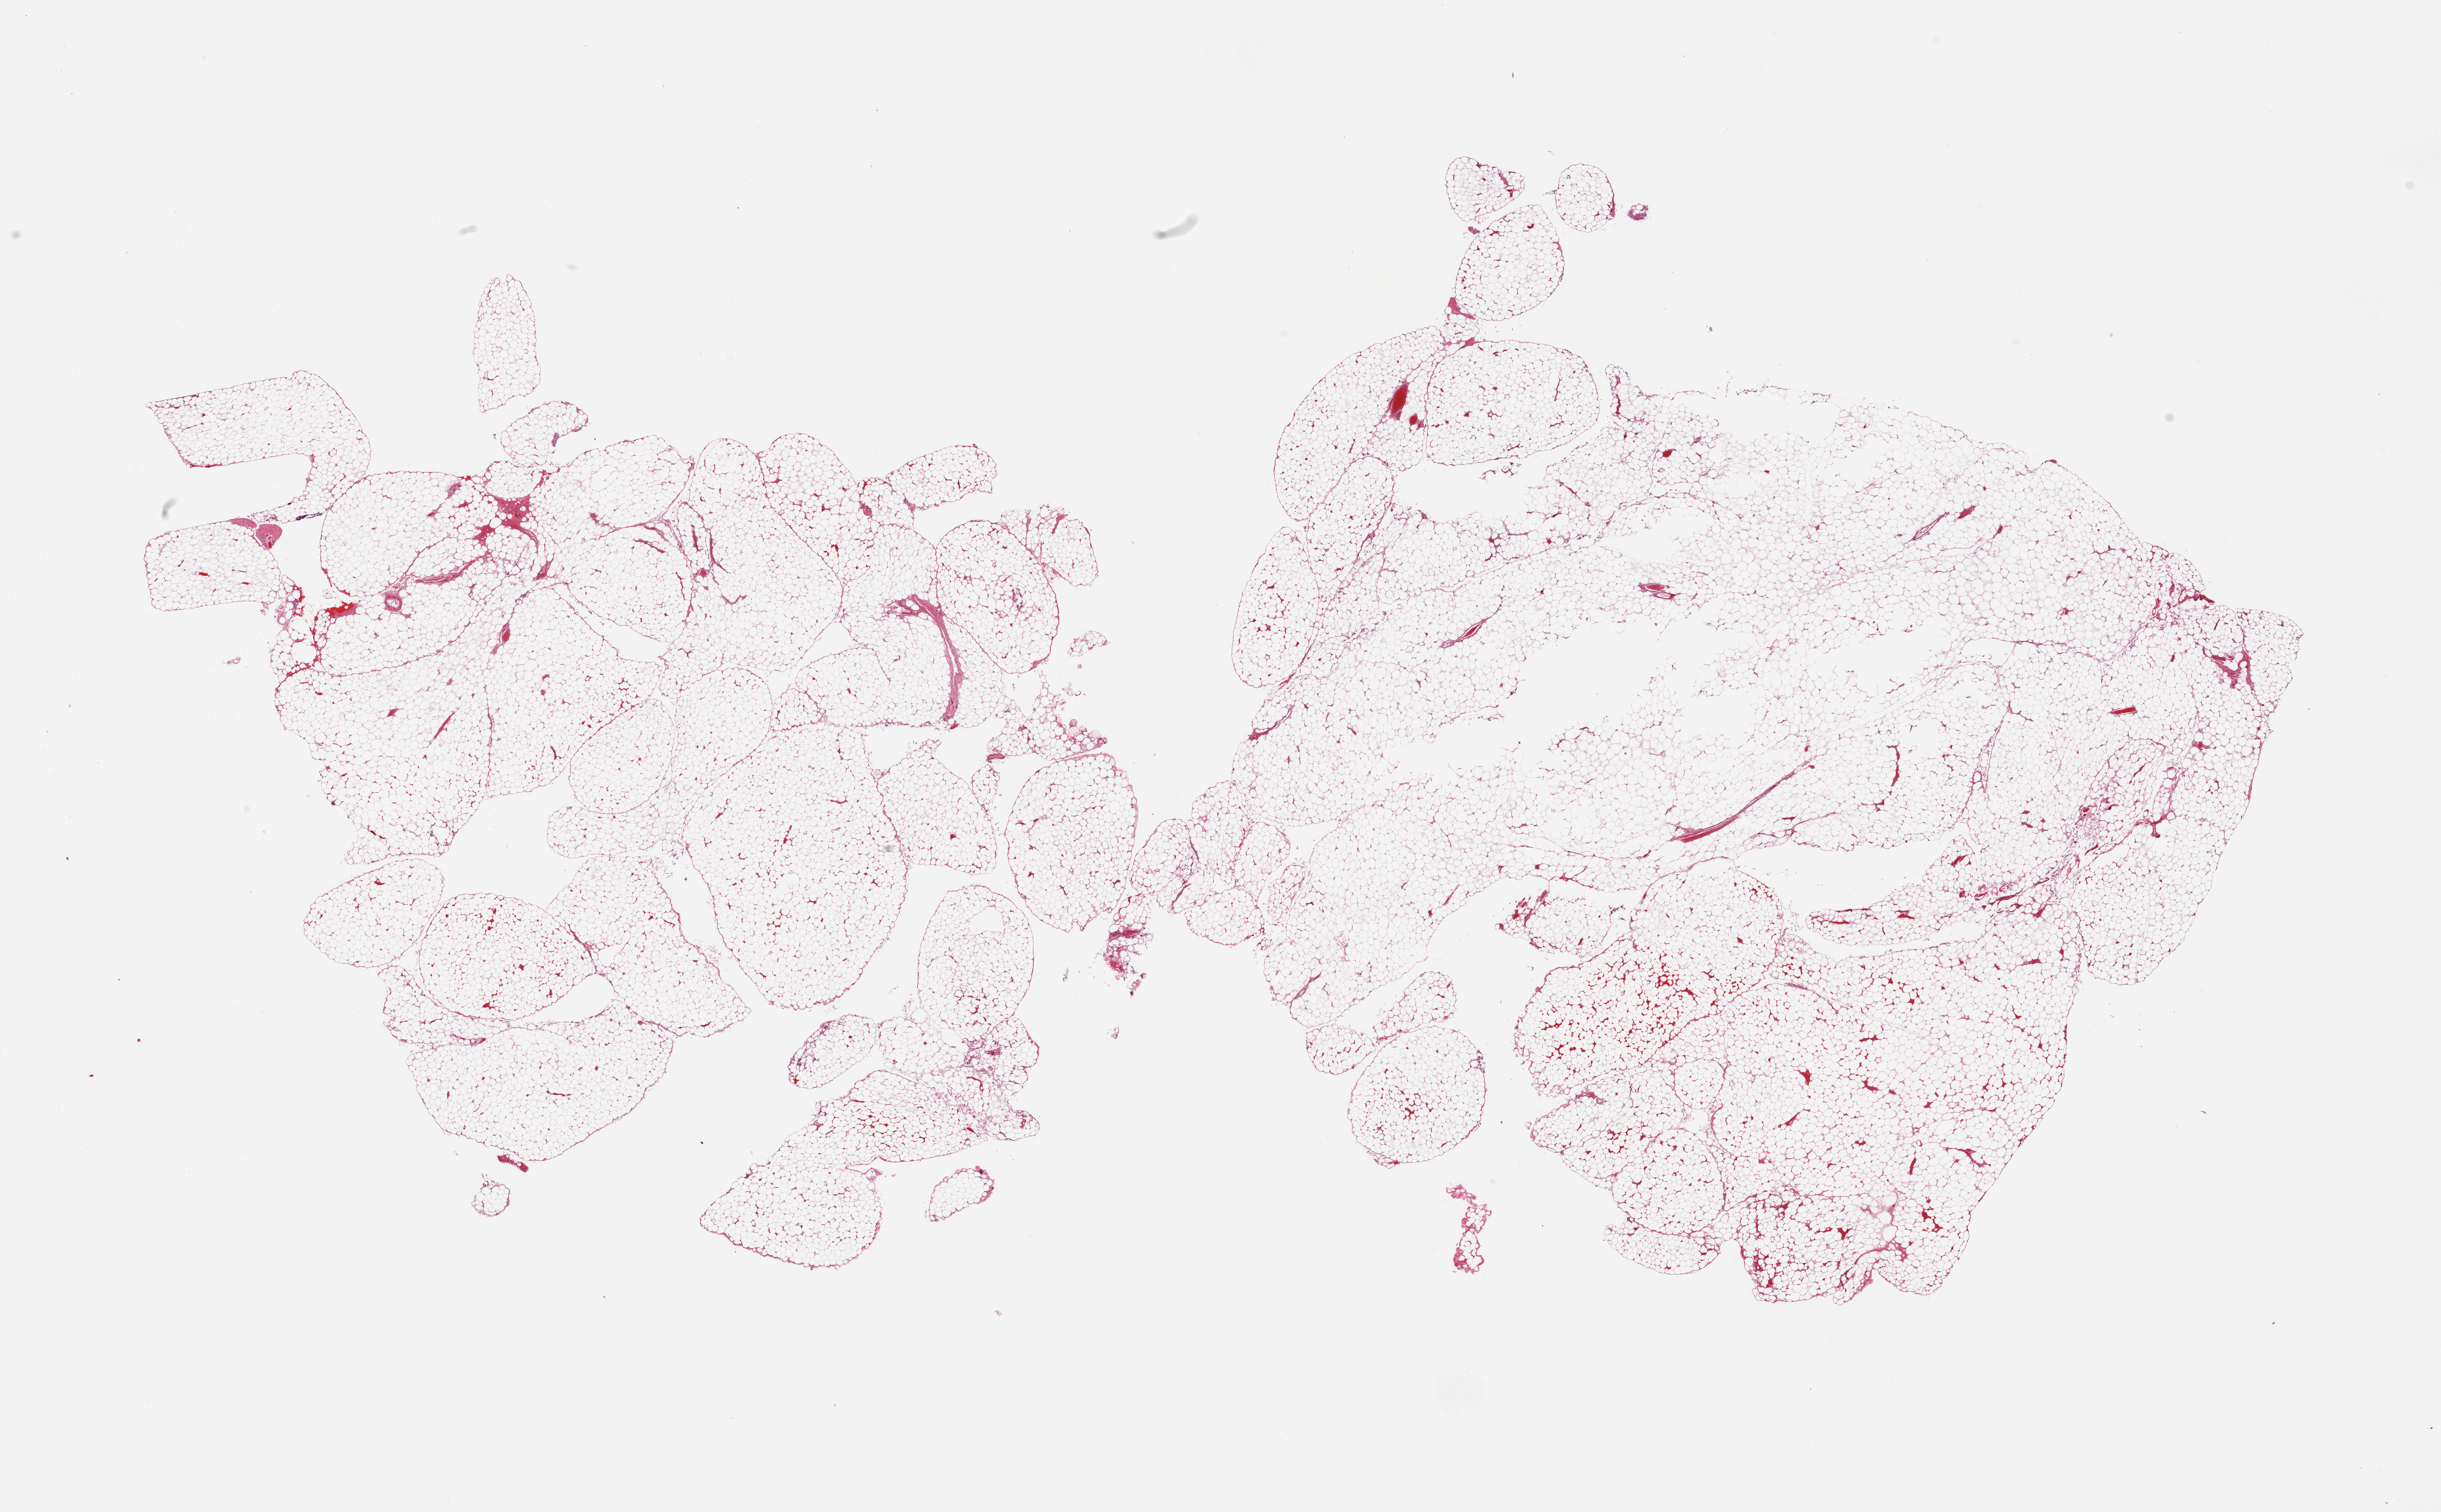
H&E whole-slide image, shown as a low-resolution overview of the whole scanned area (about 29.5 x 18.3 mm, slide scanned at 20x), PAXgene-fixed, paraffin-embedded tissue, target tissue: omentum, donor tissue sample. Donor: male.
- pathologist's review note for this sample: 2 pieces; mature adipose tissue